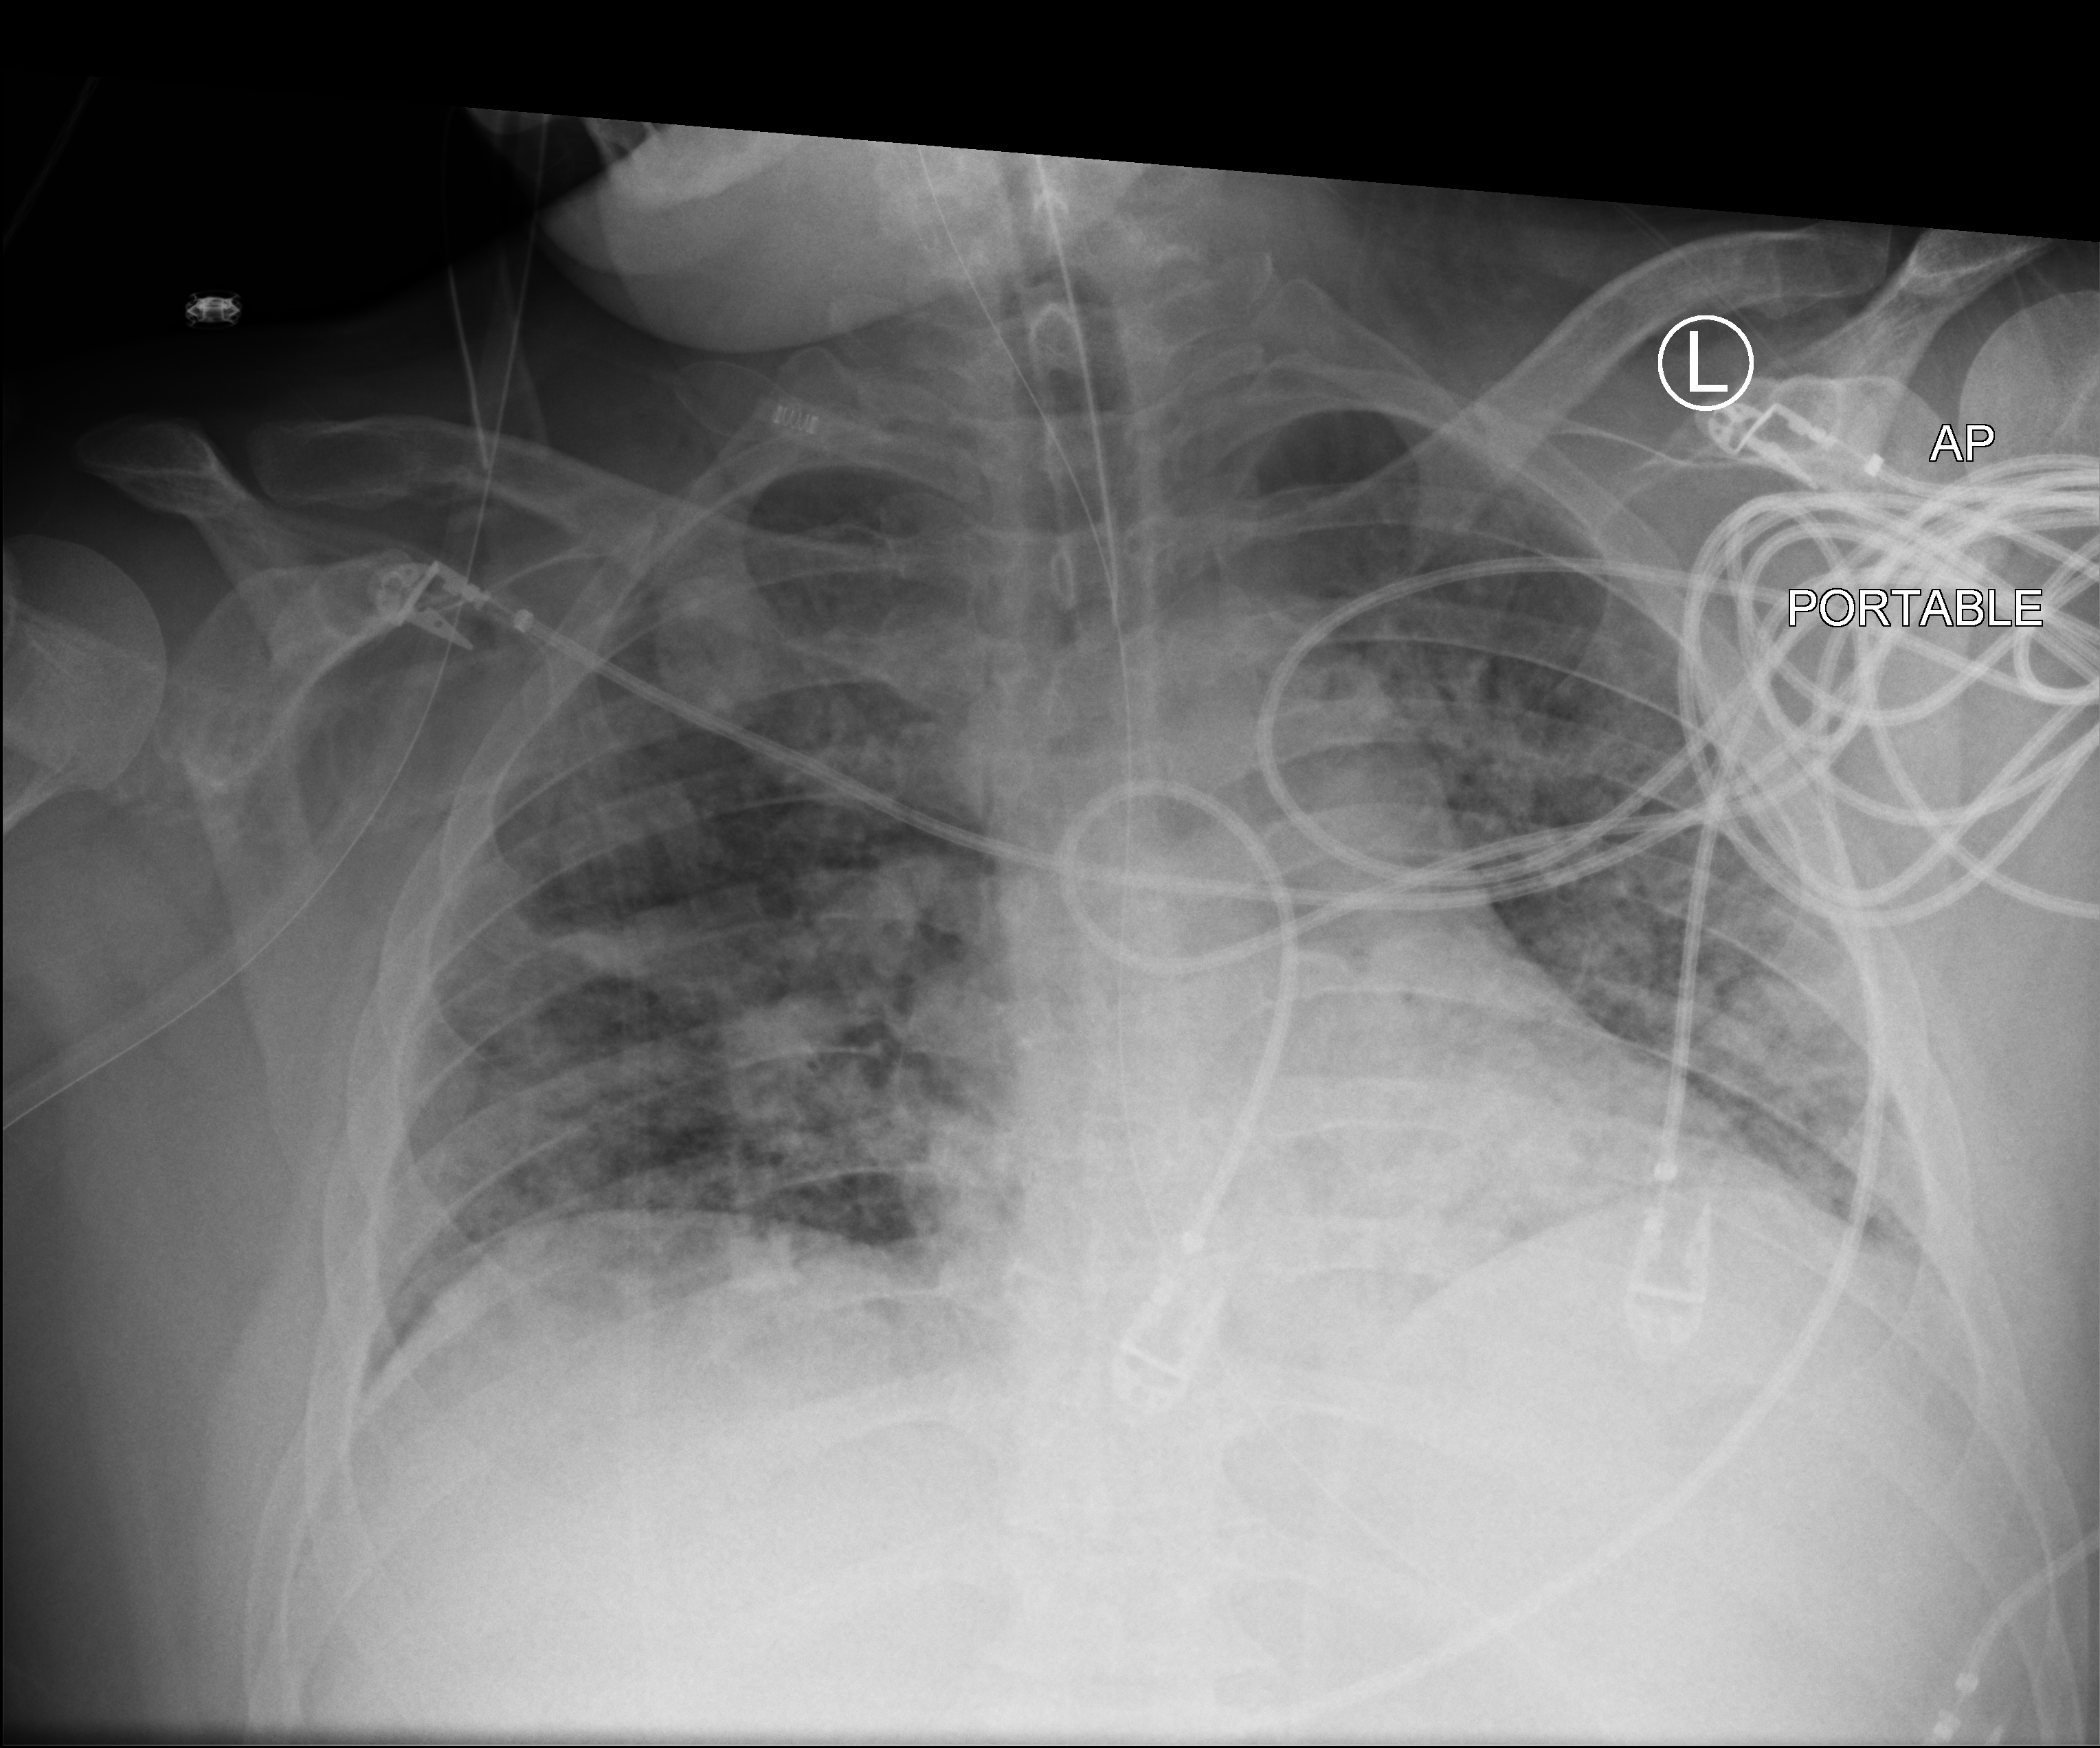
Chest X-ray (portable); anteroposterior (AP) projection. Adult patient hospitalised with COVID-19, age 18–59 years.
From the hospital-stay record, not from the radiograph (when in the stay this image was taken is not recorded):
- mechanically ventilated during this hospital stay: yes